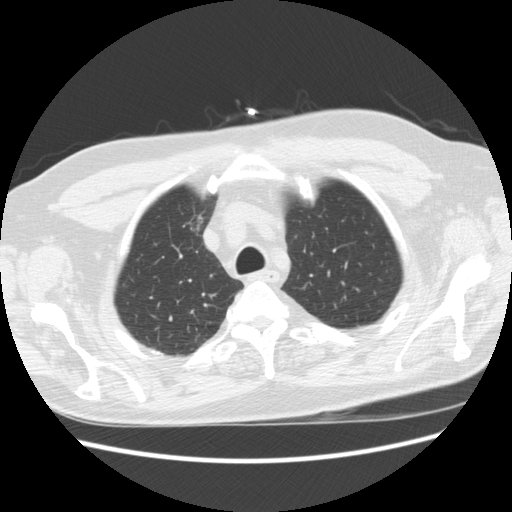
Low-dose screening chest CT, axial slice. Baseline annual screen. Lung window (W 1500 / L -600 HU). 2.5 mm slice thickness. Standard (soft-tissue) reconstruction kernel (STANDARD). Slice 48 of 241 in the series. 512 × 512 image matrix, field of view 360 × 360 mm. Male participant, aged 66 years at enrolment. Former smoker at enrolment.
- Expert reader's lesion annotation, box from (x=165, y=208) to (x=212, y=242) px.
- Screening reader's record for this exam: no non-calcified nodule ≥4 mm recorded.
- Lung cancer was diagnosed 951 days after this screen: bronchiolo-alveolar adenocarcinoma, NOS, right upper lobe, moderately differentiated (G2), stage IA (AJCC 6th edition), 12 mm at pathology.